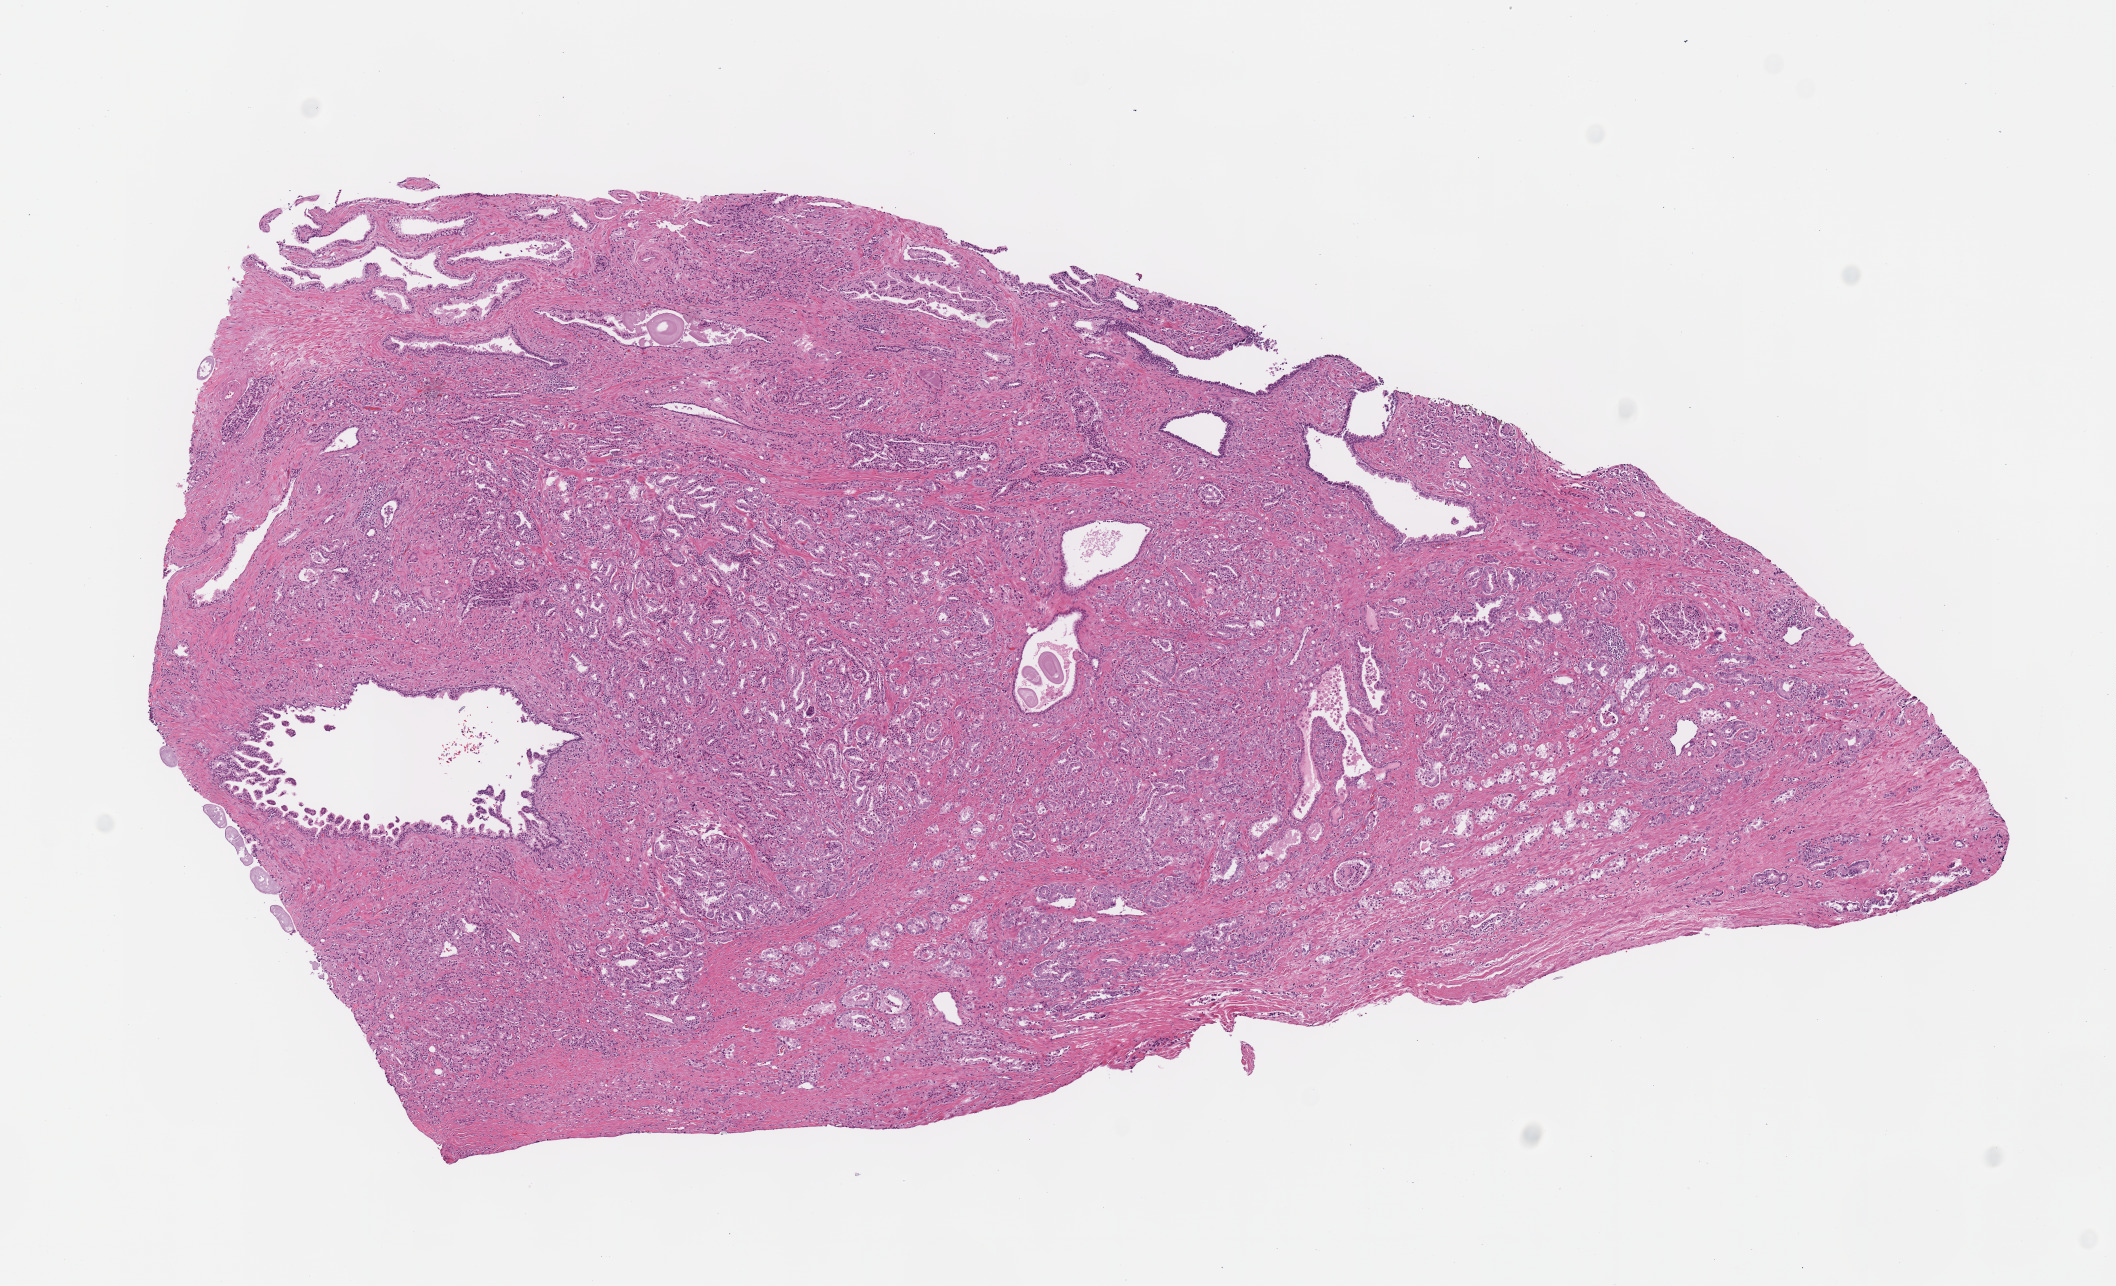
H&E whole-slide image — low-resolution overview of the scanned area, about 8.3 x 5.1 mm (slide scanned at 40x). FFPE section. Primary tumour sample from the prostate. Male, age 58 years at initial diagnosis. Gleason score: 7 (4+3).
Diagnosis: Acinar cell carcinoma (prostate gland). Lymph nodes positive (case pathology): 0 of 3 examined.